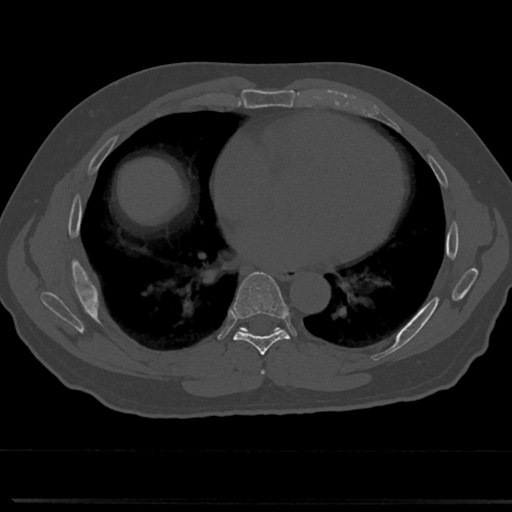
CT including the spine, one axial slice; position 397 of 817 along the scan axis; reconstruction kernel Br40s/3; 120 kVp; bone window (W 1800 / L 400 HU); 0.5 mm slice thickness; 512 × 512 image matrix. Patient: male, 61 years. Case-level facts recorded for this patient, not image findings: primary cancer: prostate.
Outlined on this slice (semi-automatic segmentation, software-assisted and operator-edited):
- T6 vertebra: box from (x=261, y=340) to (x=319, y=377) px
- T7 vertebra: (x=214, y=275)–(x=310, y=358)